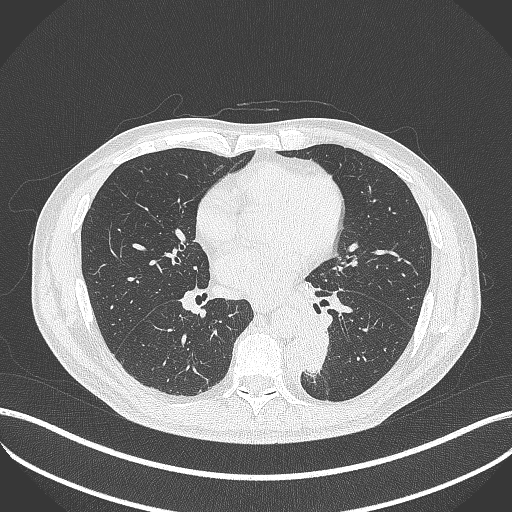
Chest CT, one axial slice; 120 kVp; lung window (W 1500 / L -600 HU); 512 × 512 image matrix, field of view 400 × 400 mm. Male patient, age 72 years. Case-level facts recorded for this patient, not image findings: clinical TNM (as recorded): T2b N0 M1.
Structures marked on this image (rectangle marked by the reading radiologist):
- lung tumour (recorded histology: adenocarcinoma): bounding box (x1, y1, x2, y2) in pixels: (299, 328, 333, 379)